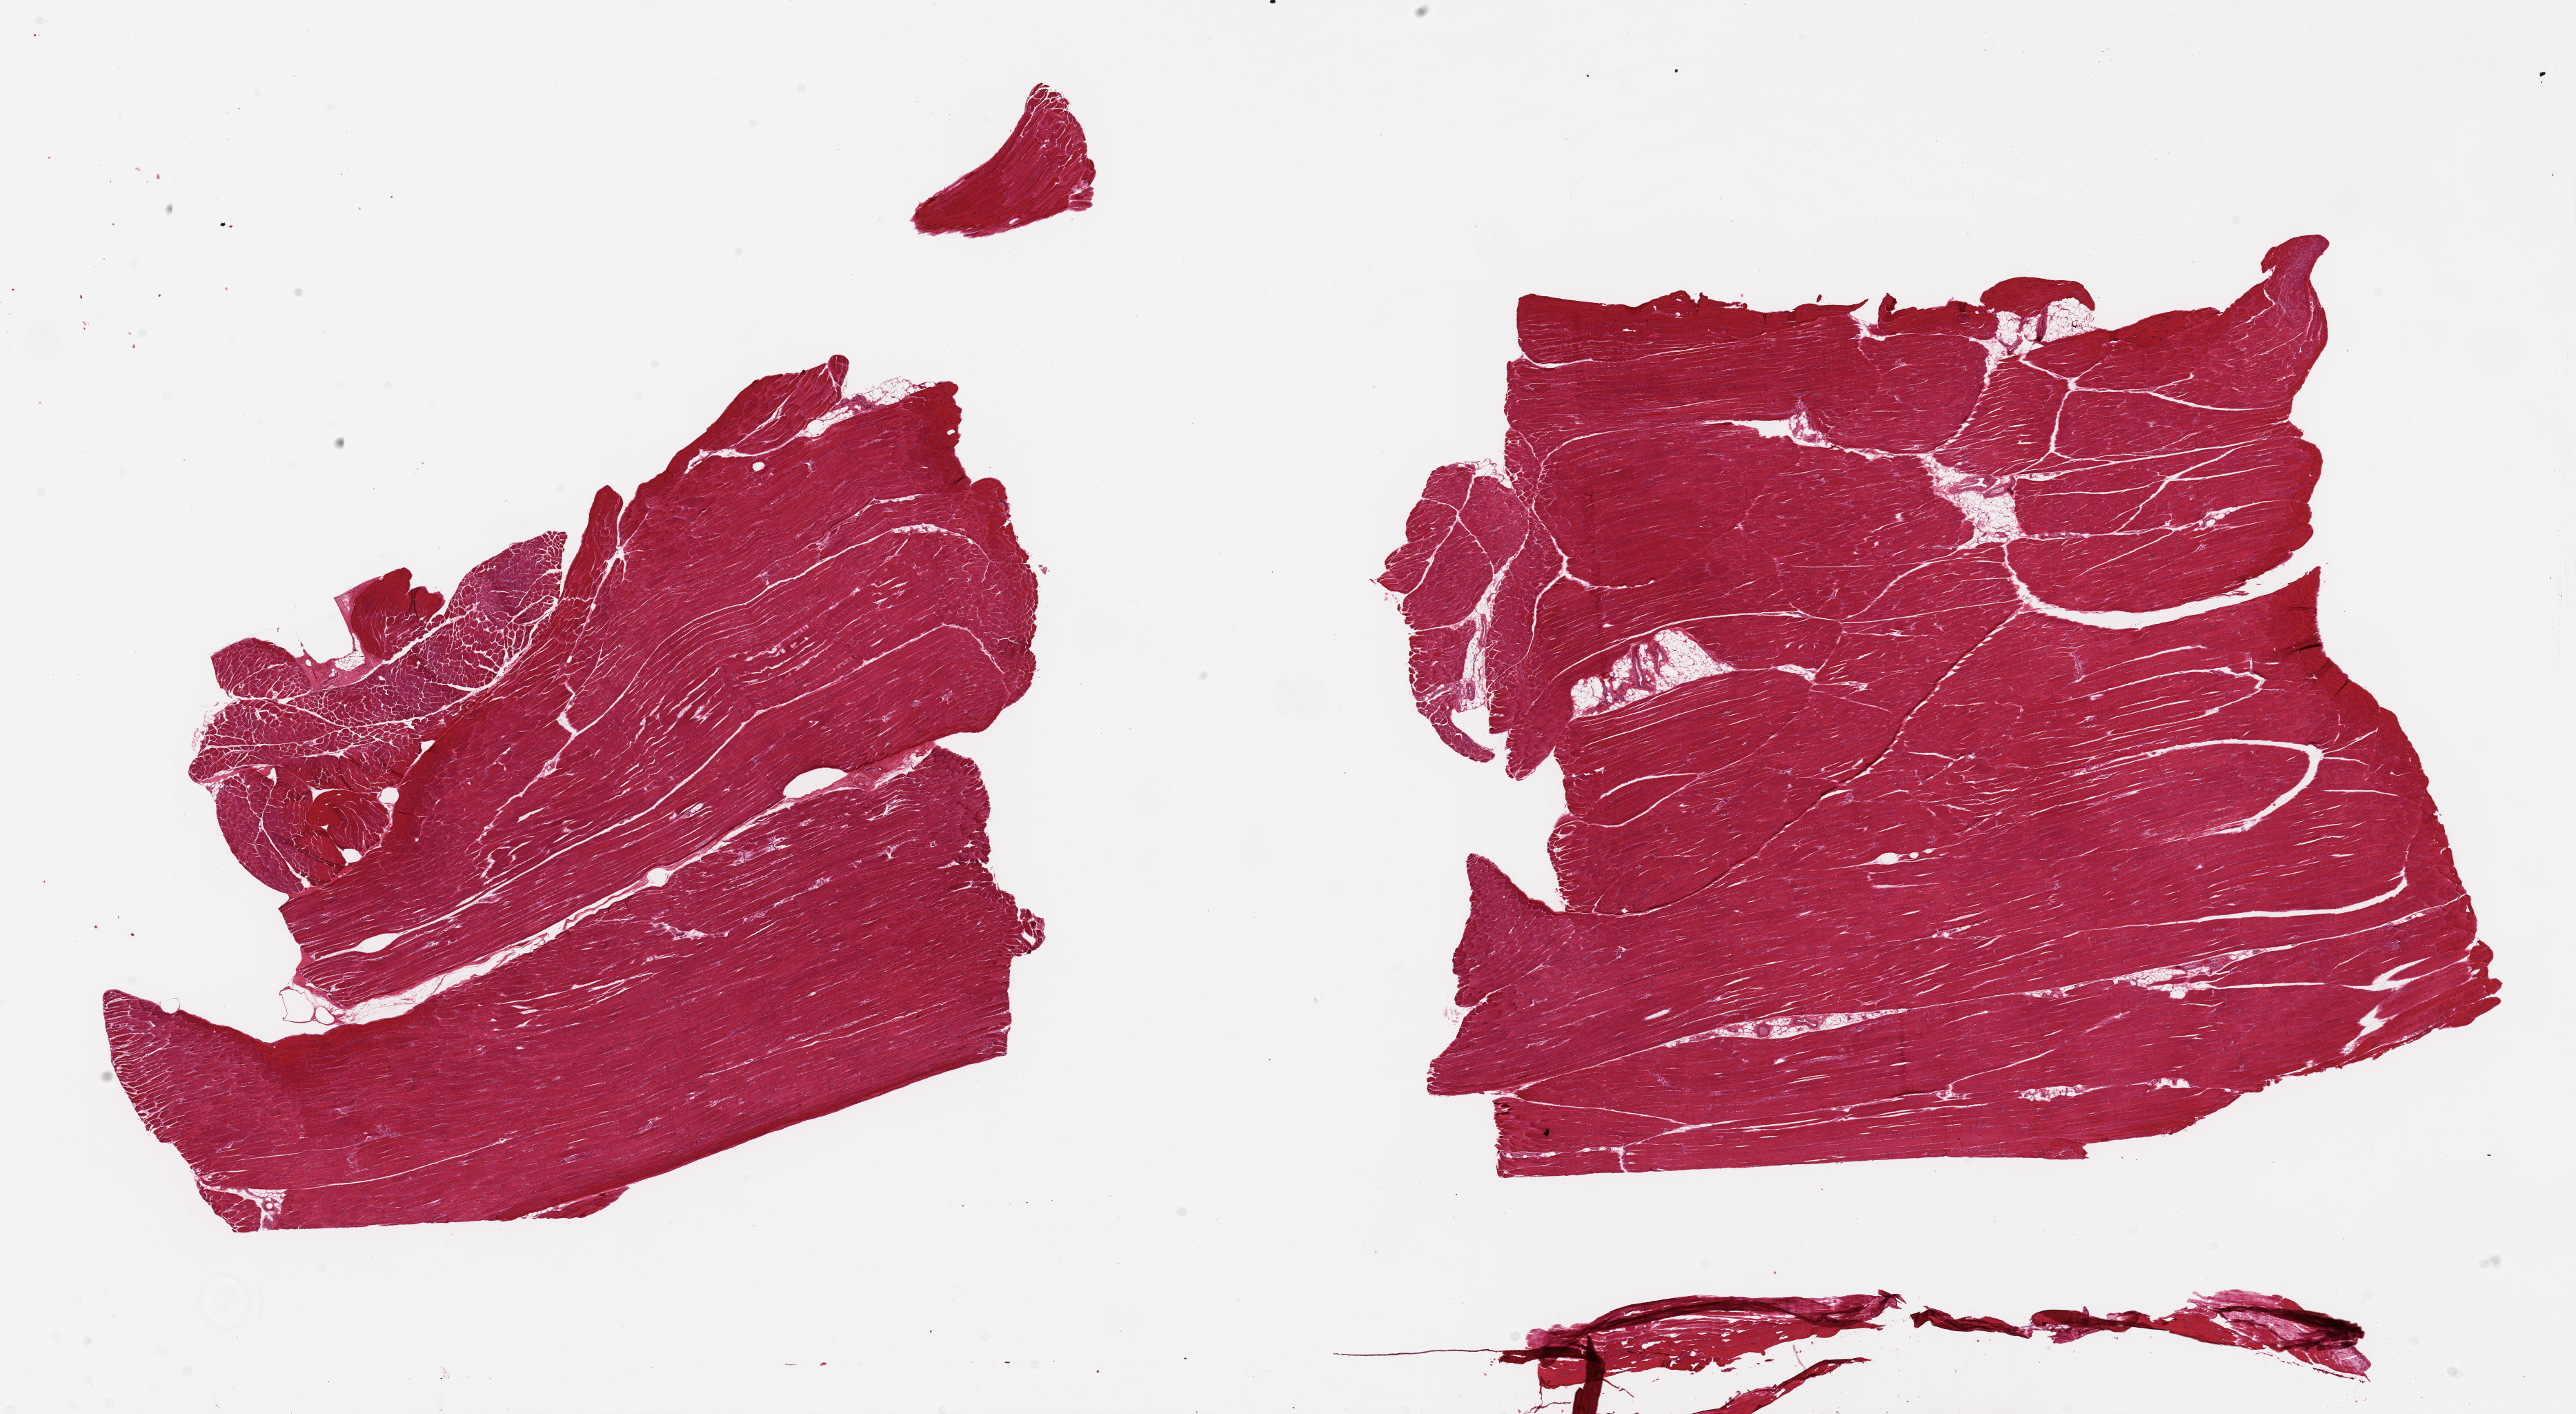
Digitized H&E-stained section, whole scanned area (about 29.5 x 16.2 mm) shown as a low-resolution overview. PAXgene-fixed paraffin-embedded (PFPE) section. Sampled site (target tissue): skeletal muscle. Donor tissue sample. Donor: male.
* reviewer comment on this tissue sample: 2 pieces, minimal interstitial fat